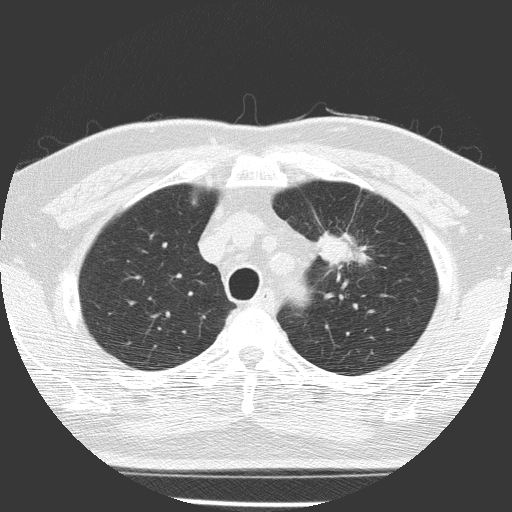
Low-dose screening chest CT, one axial slice; slice 120 of 156 in the series (ordered by position); reconstruction kernel FC51; lung window (W 1500 / L -600 HU); 512 × 512 image matrix, field of view 309 × 309 mm.
Annotated regions visible in this slice (manually delineated by an expert):
- lesion 1 (tumor, upper lobe of left lung): bounding box (x1, y1, x2, y2) in pixels: (318, 233, 366, 268)